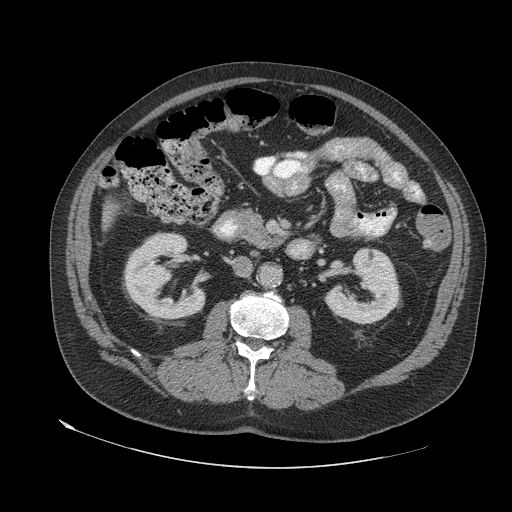
Contrast-enhanced abdominal CT (liver protocol), one axial slice; slice 13 of 79 in the series (ordered by position); reconstruction kernel STANDARD; 140 kVp; soft-tissue window (W 400 / L 40 HU); 2.5 mm slice thickness; 512 × 512 image matrix, field of view 480 × 480 mm. Case-level facts recorded for this patient, not image findings: diagnosis: hepatocellular carcinoma (patient treated with transarterial chemoembolisation; whether this scan precedes or follows treatment is not stated here); TNM stage (as recorded): Stage-IVA; Child-Pugh class: A; tumour differentiation: well differentiated.
Annotated regions visible in this slice (semi-automatically segmented with operator editing):
- liver parenchyma outside the tumour (the mass and vessels are separate outlines, so this box may not span the whole liver): bounding box <102,203,114,230> (left, top, right, bottom; pixels)